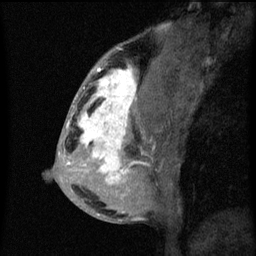
Breast MRI (dynamic contrast-enhanced), one sagittal slice; slice 27 of 60 in the series (ordered by position); dynamic contrast-enhanced series, image 2 of 3 at this slice position (ordered by acquisition); 1.5 T; TE 4.2 ms, TR 8 ms; 2 mm slice thickness; 256 × 256 image matrix, field of view 180 × 180 mm. Female patient, age 50 years.
Structures marked on this image (semi-automatic segmentation, software-assisted and operator-edited):
- analysis volume of interest (the breast-tissue region the enhancement analysis was run in; not a lesion): bounding box [x1, y1, x2, y2] px = [66, 64, 141, 187]
- tumour enhancement mask (voxels above the 70 % enhancement threshold inside the analysis volume of interest): [66, 66, 137, 185]